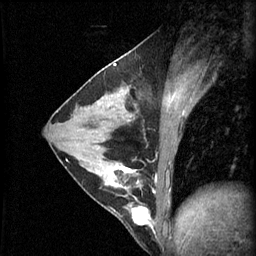
Breast MRI (dynamic contrast-enhanced), one sagittal slice; position 29 of 60 along the scan axis; 3 images stored at this slice position (order not interpretable as contrast timing); 1.5 T; TE 4.2 ms, TR 11 ms; 256 × 256 image matrix, field of view 180 × 180 mm. Patient: female, 29 years.
Annotated regions visible in this slice (semi-automatically segmented with operator editing):
- analysis volume of interest (the breast-tissue region the enhancement analysis was run in; not a lesion): bounding box [x1, y1, x2, y2] px = [93, 164, 153, 229]
- tumour enhancement mask (voxels above the 70 % enhancement threshold inside the analysis volume of interest): [105, 166, 153, 229]